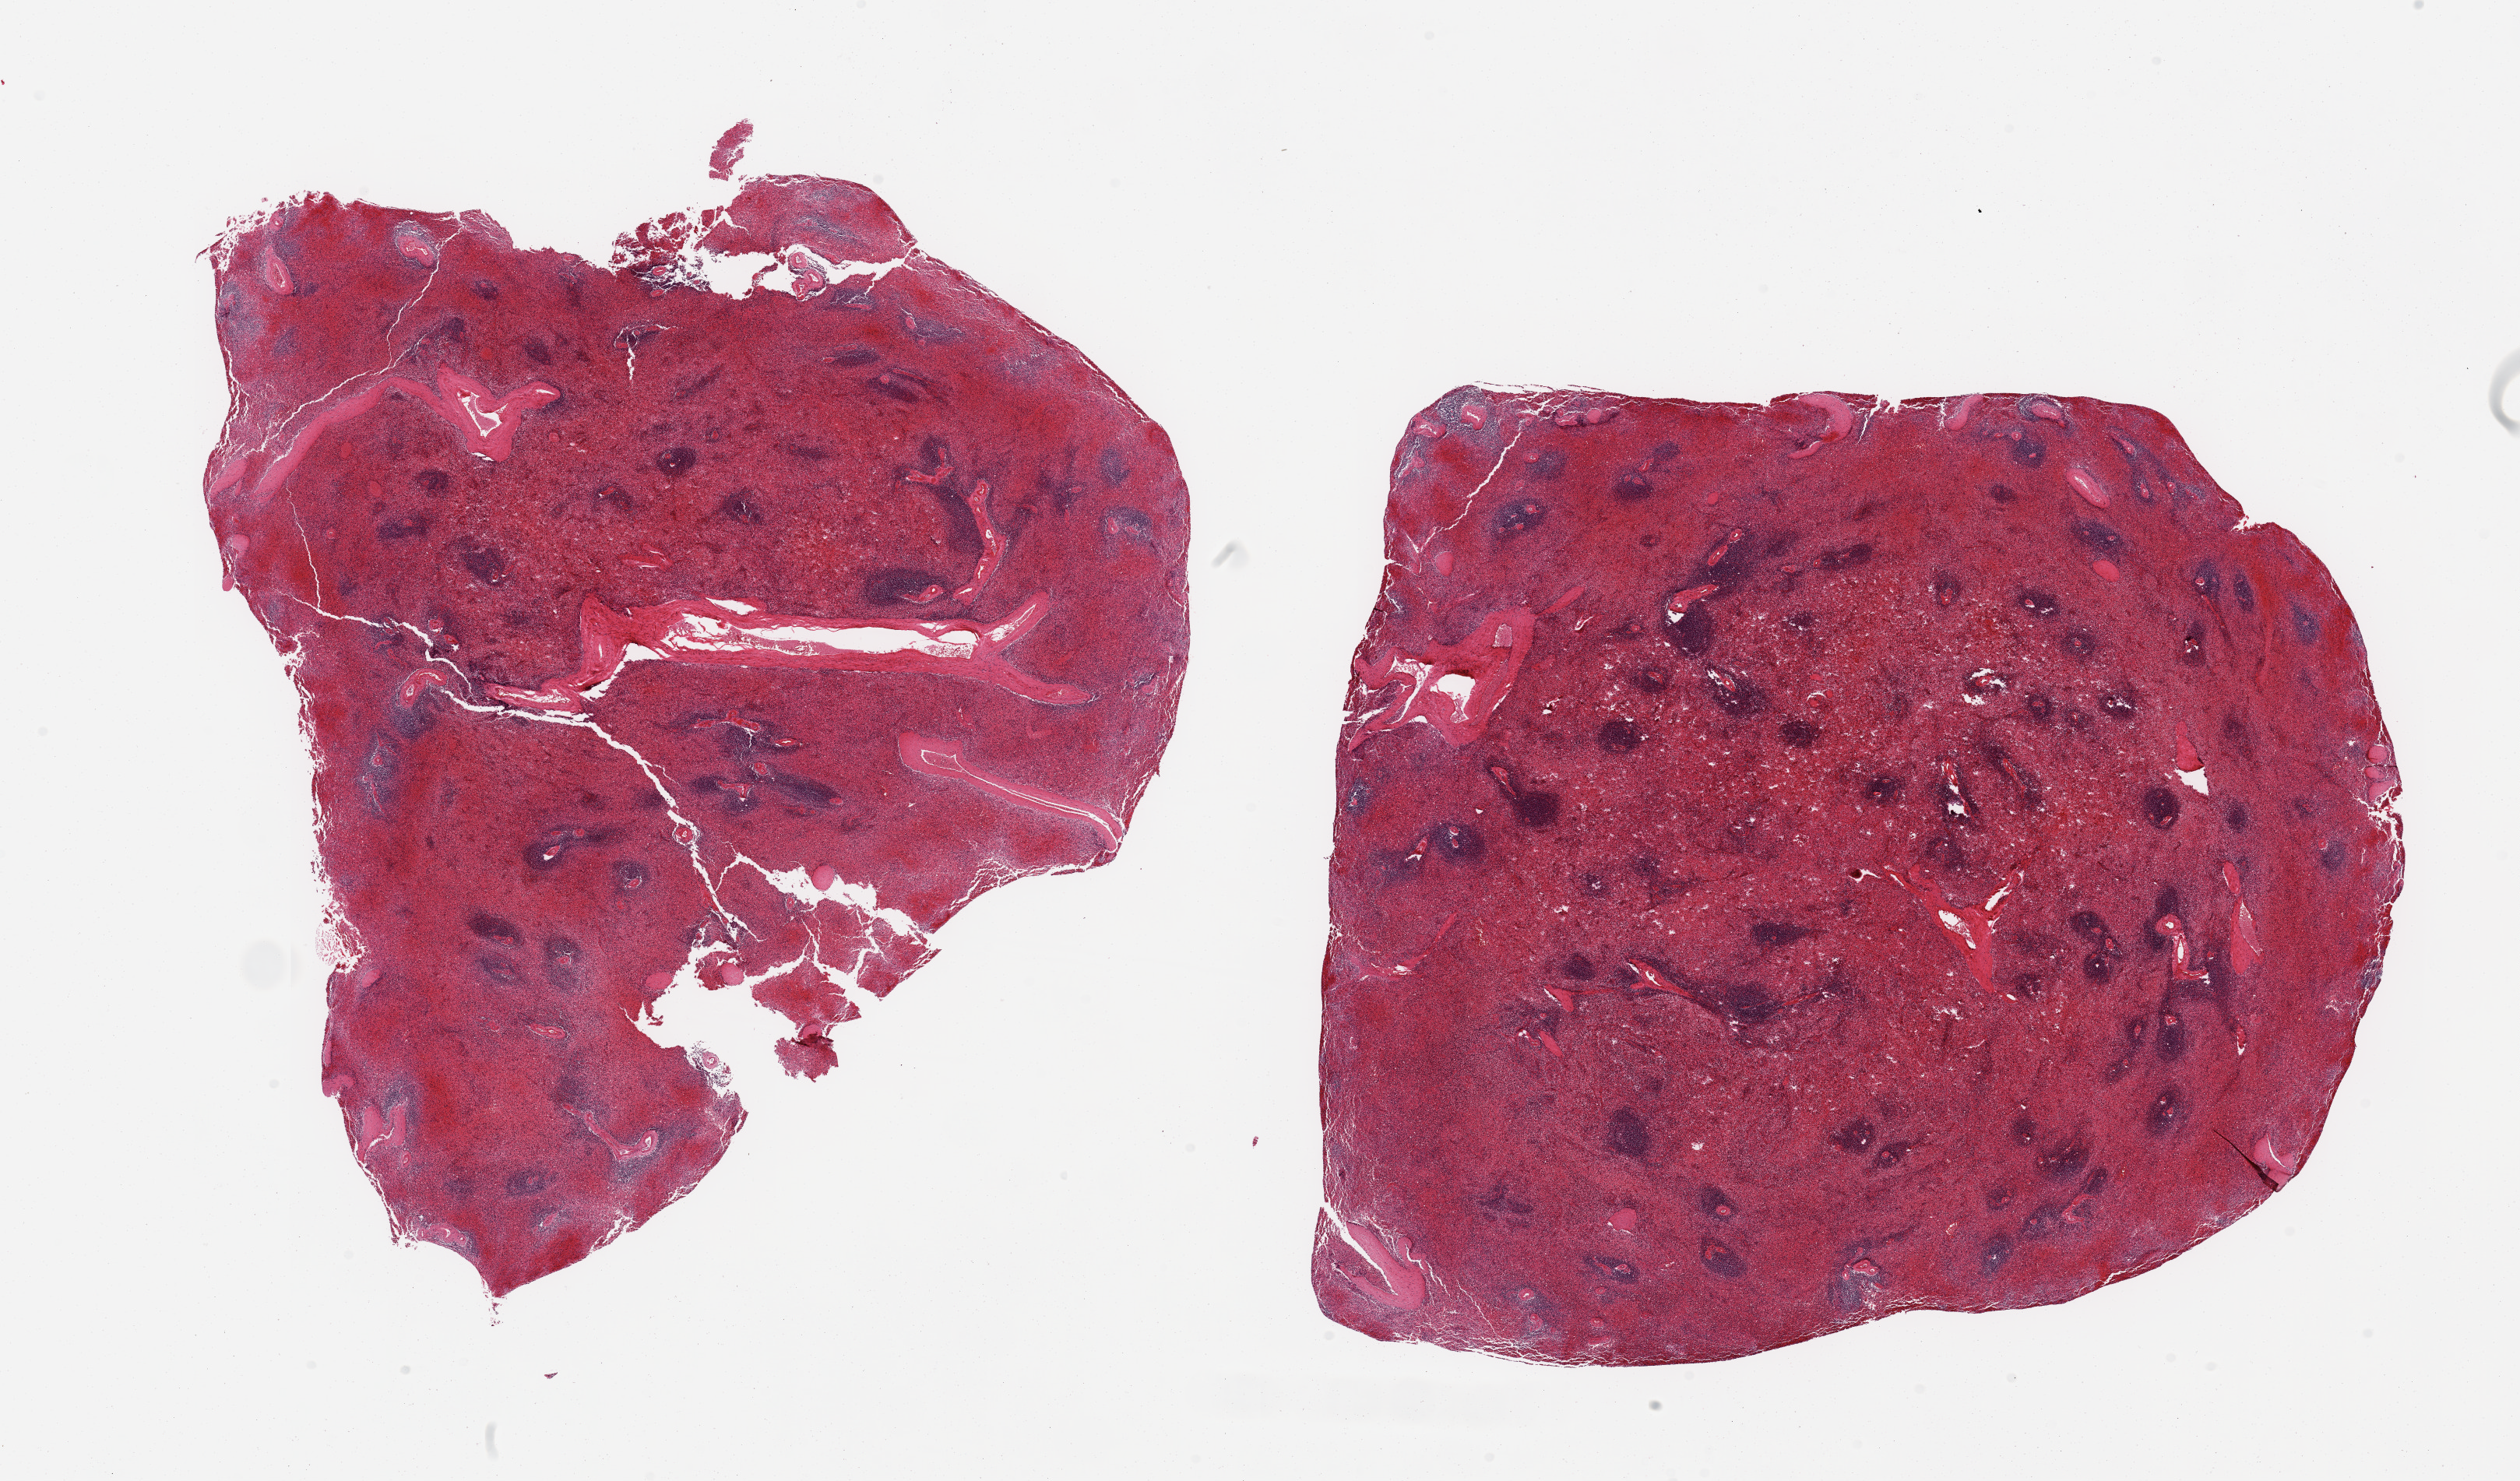
Digitized haematoxylin and eosin-stained section — whole scanned area (about 25.6 x 15.0 mm) shown as a low-resolution overview; PAXgene-fixed paraffin-embedded (PFPE) section; sampled site (target tissue): spleen; donor tissue sample. Donor sex: male.
Review note (as recorded): 2 pieces, marked congestion.